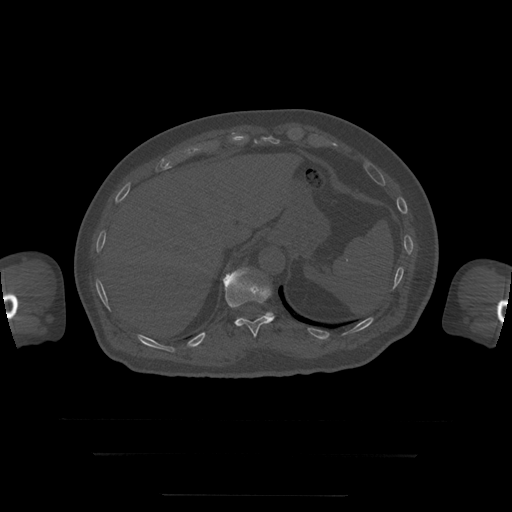
CT including the spine, one axial slice; slice 95 of 397 in the series (ordered by position); 120 kVp; bone window (W 1800 / L 400 HU); 1.25 mm slice thickness; 512 × 512 image matrix, field of view 510 × 510 mm. Patient age 73 years. From the clinical record (not read from this slice): primary cancer: prostate.
Structures marked on this image (semi-automatically segmented with operator editing):
- T11 vertebra: box from (x=223, y=268) to (x=275, y=338) px
- T12 vertebra: (x=238, y=312)–(x=274, y=319)